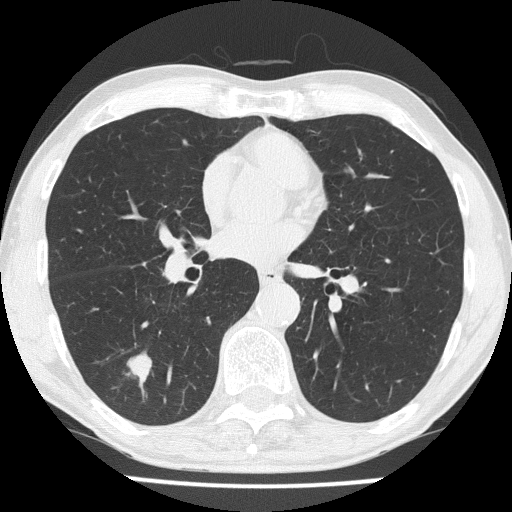
Chest CT (low-dose screening protocol), one axial image, third annual screen, lung window (W 1500 / L -600 HU), lung (sharp) reconstruction kernel (FC51), slice 106 of 186 in the series, 512 × 512 image matrix. Male participant, aged 59 years at enrolment. Former smoker at enrolment.
Expert-annotated lung lesion, box from (x=112, y=346) to (x=160, y=393) px. Screening reader's record for this exam (one nodule recorded; not confirmed to be the boxed lesion): non-calcified nodule or mass ≥4 mm, right lower lobe, 20 × 16 mm, smooth margins, soft tissue attenuation, pre-existing on the prior screen: no. Official screen result: positive, other. Lung cancer was diagnosed 25 days after this screen: small cell carcinoma, NOS, right lower lobe, stage IIA (AJCC 6th edition), 20 mm at pathology.